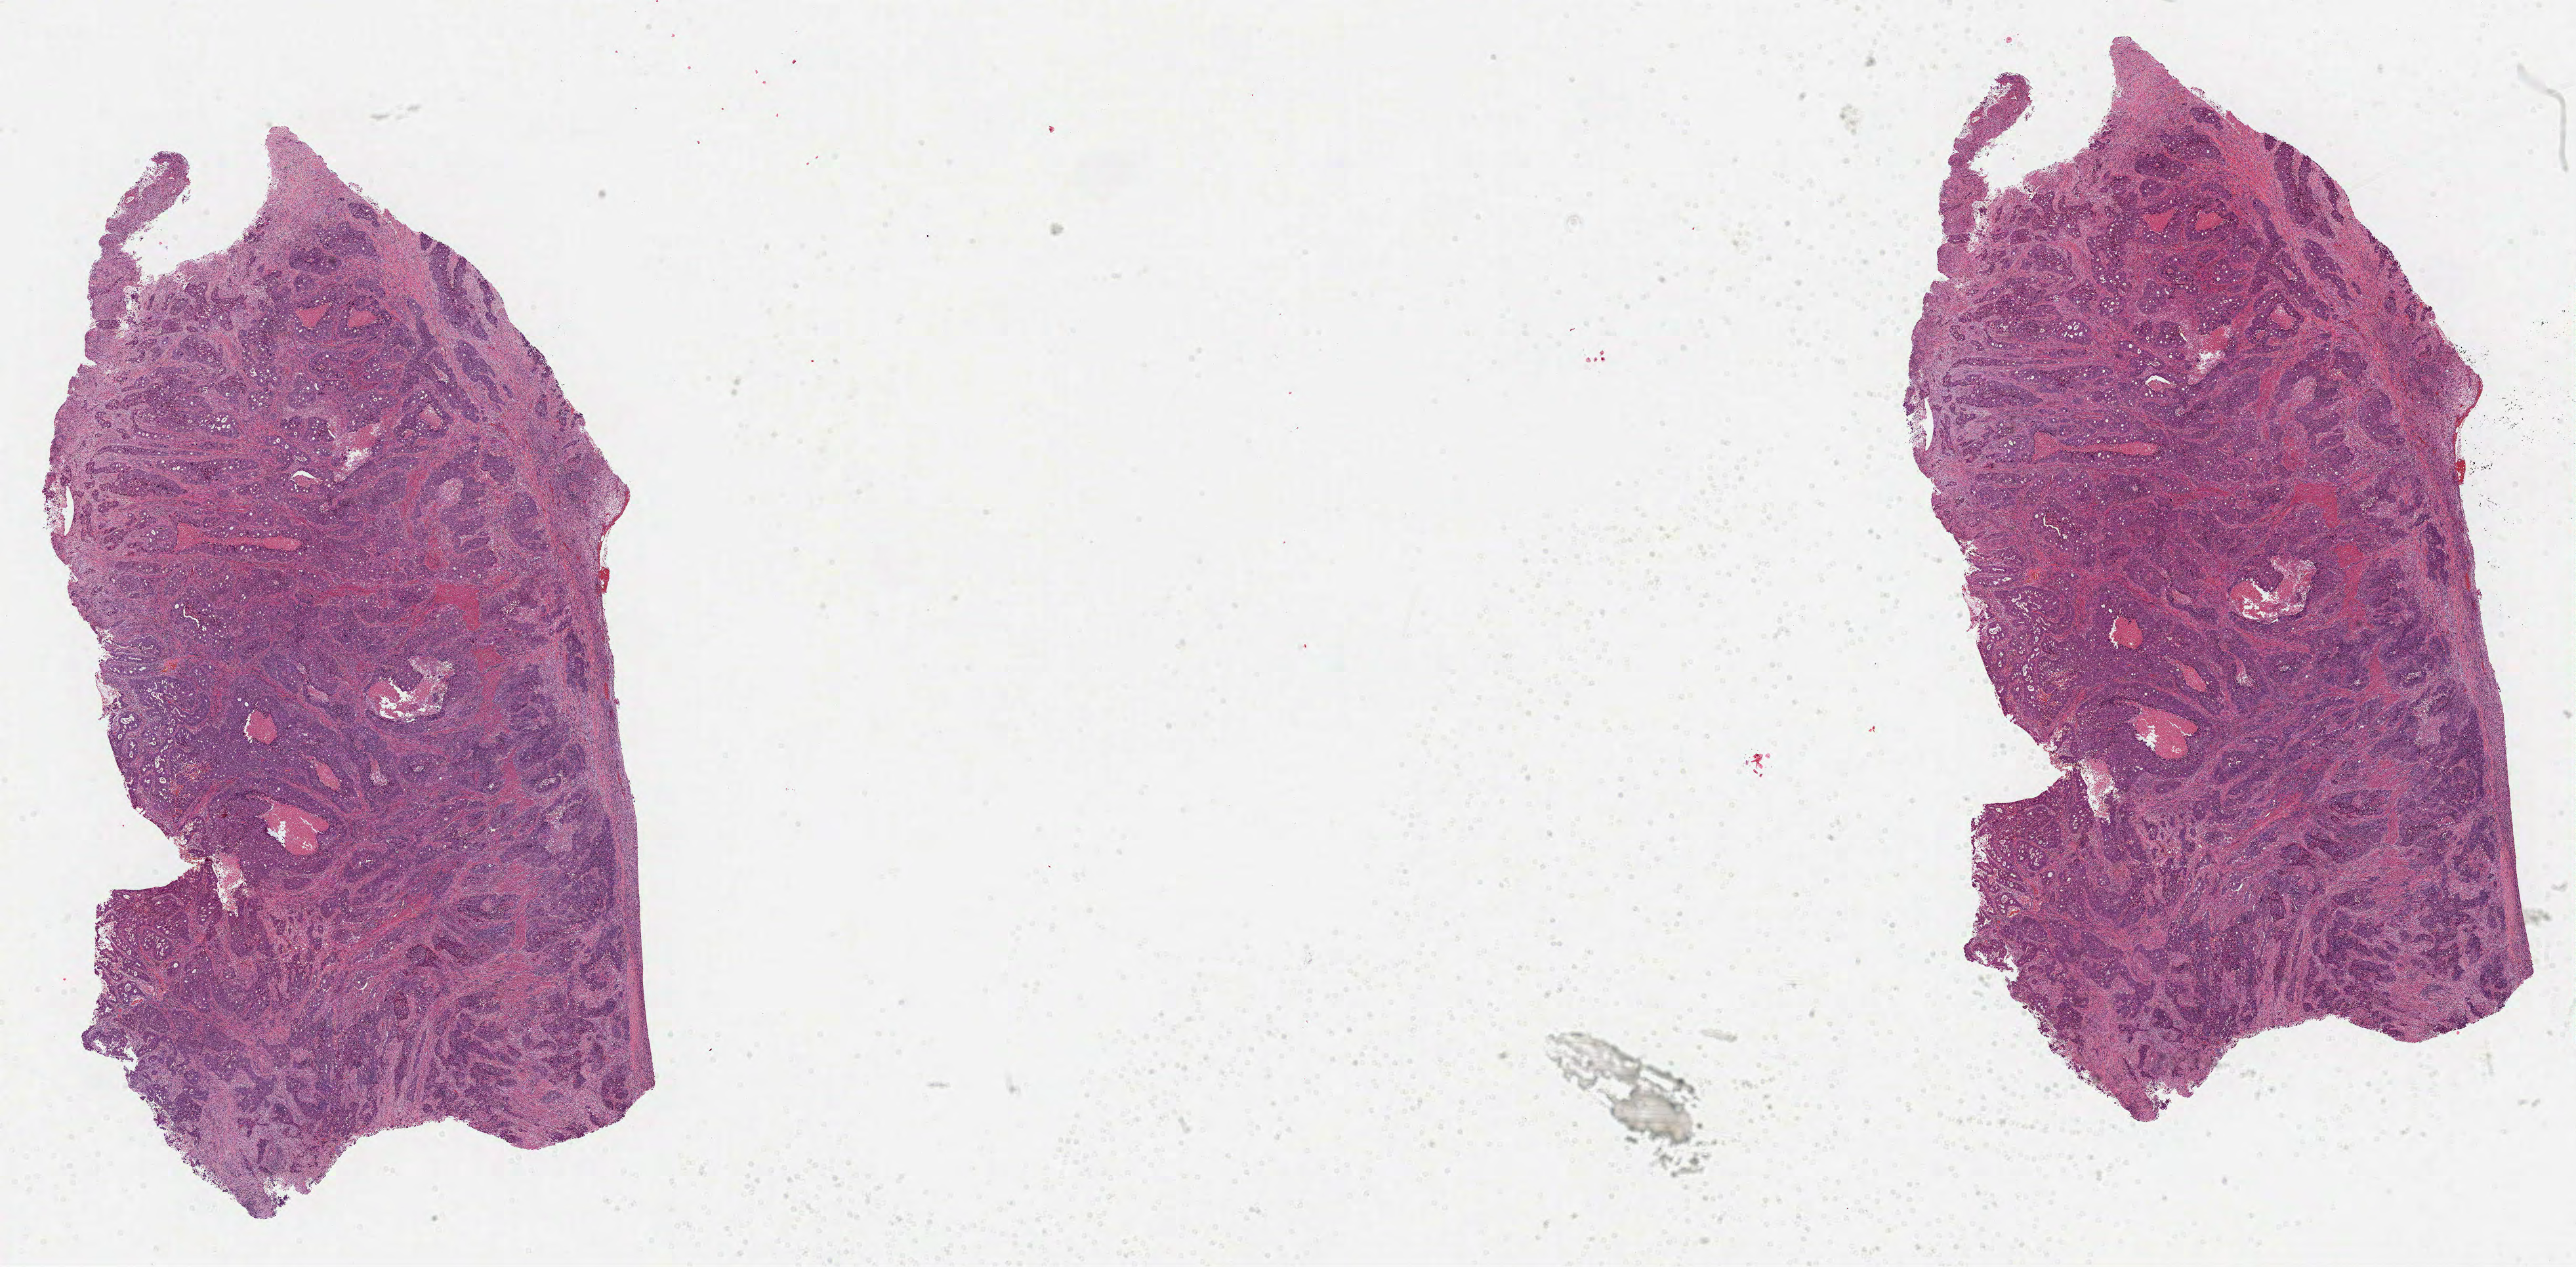
Whole-slide histology image, H&E, a low-resolution overview of the entire scanned area, about 31.7 x 15.6 mm (slide scanned at 40x), formalin-fixed paraffin-embedded (FFPE) diagnostic section, colon, primary tumour sample. Female patient; age at initial diagnosis 81 years.
Histologic diagnosis: Adenocarcinoma, NOS.